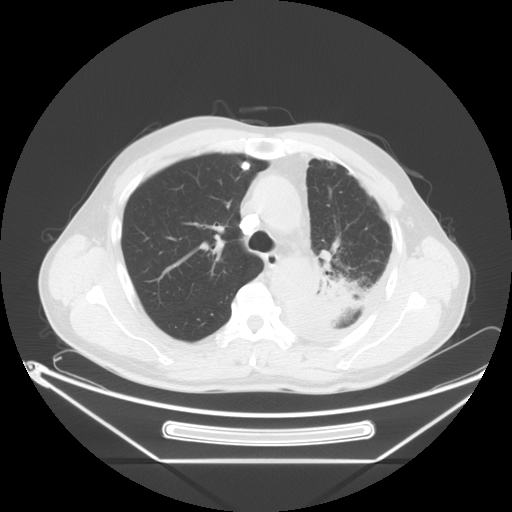
Chest CT, one axial slice. Position 43 of 63 along the scan axis. 120 kVp. Lung window (W 1500 / L -600 HU). 512 × 512 image matrix, field of view 442 × 442 mm. Male patient, age 60 years. From the clinical record (not read from this slice): clinical TNM (as recorded): T4 N1 M1.
Outlined on this slice (rectangle marked by the reading radiologist):
- lung tumour (recorded histology: adenocarcinoma): bounding box <309,256,358,333> (left, top, right, bottom; pixels)